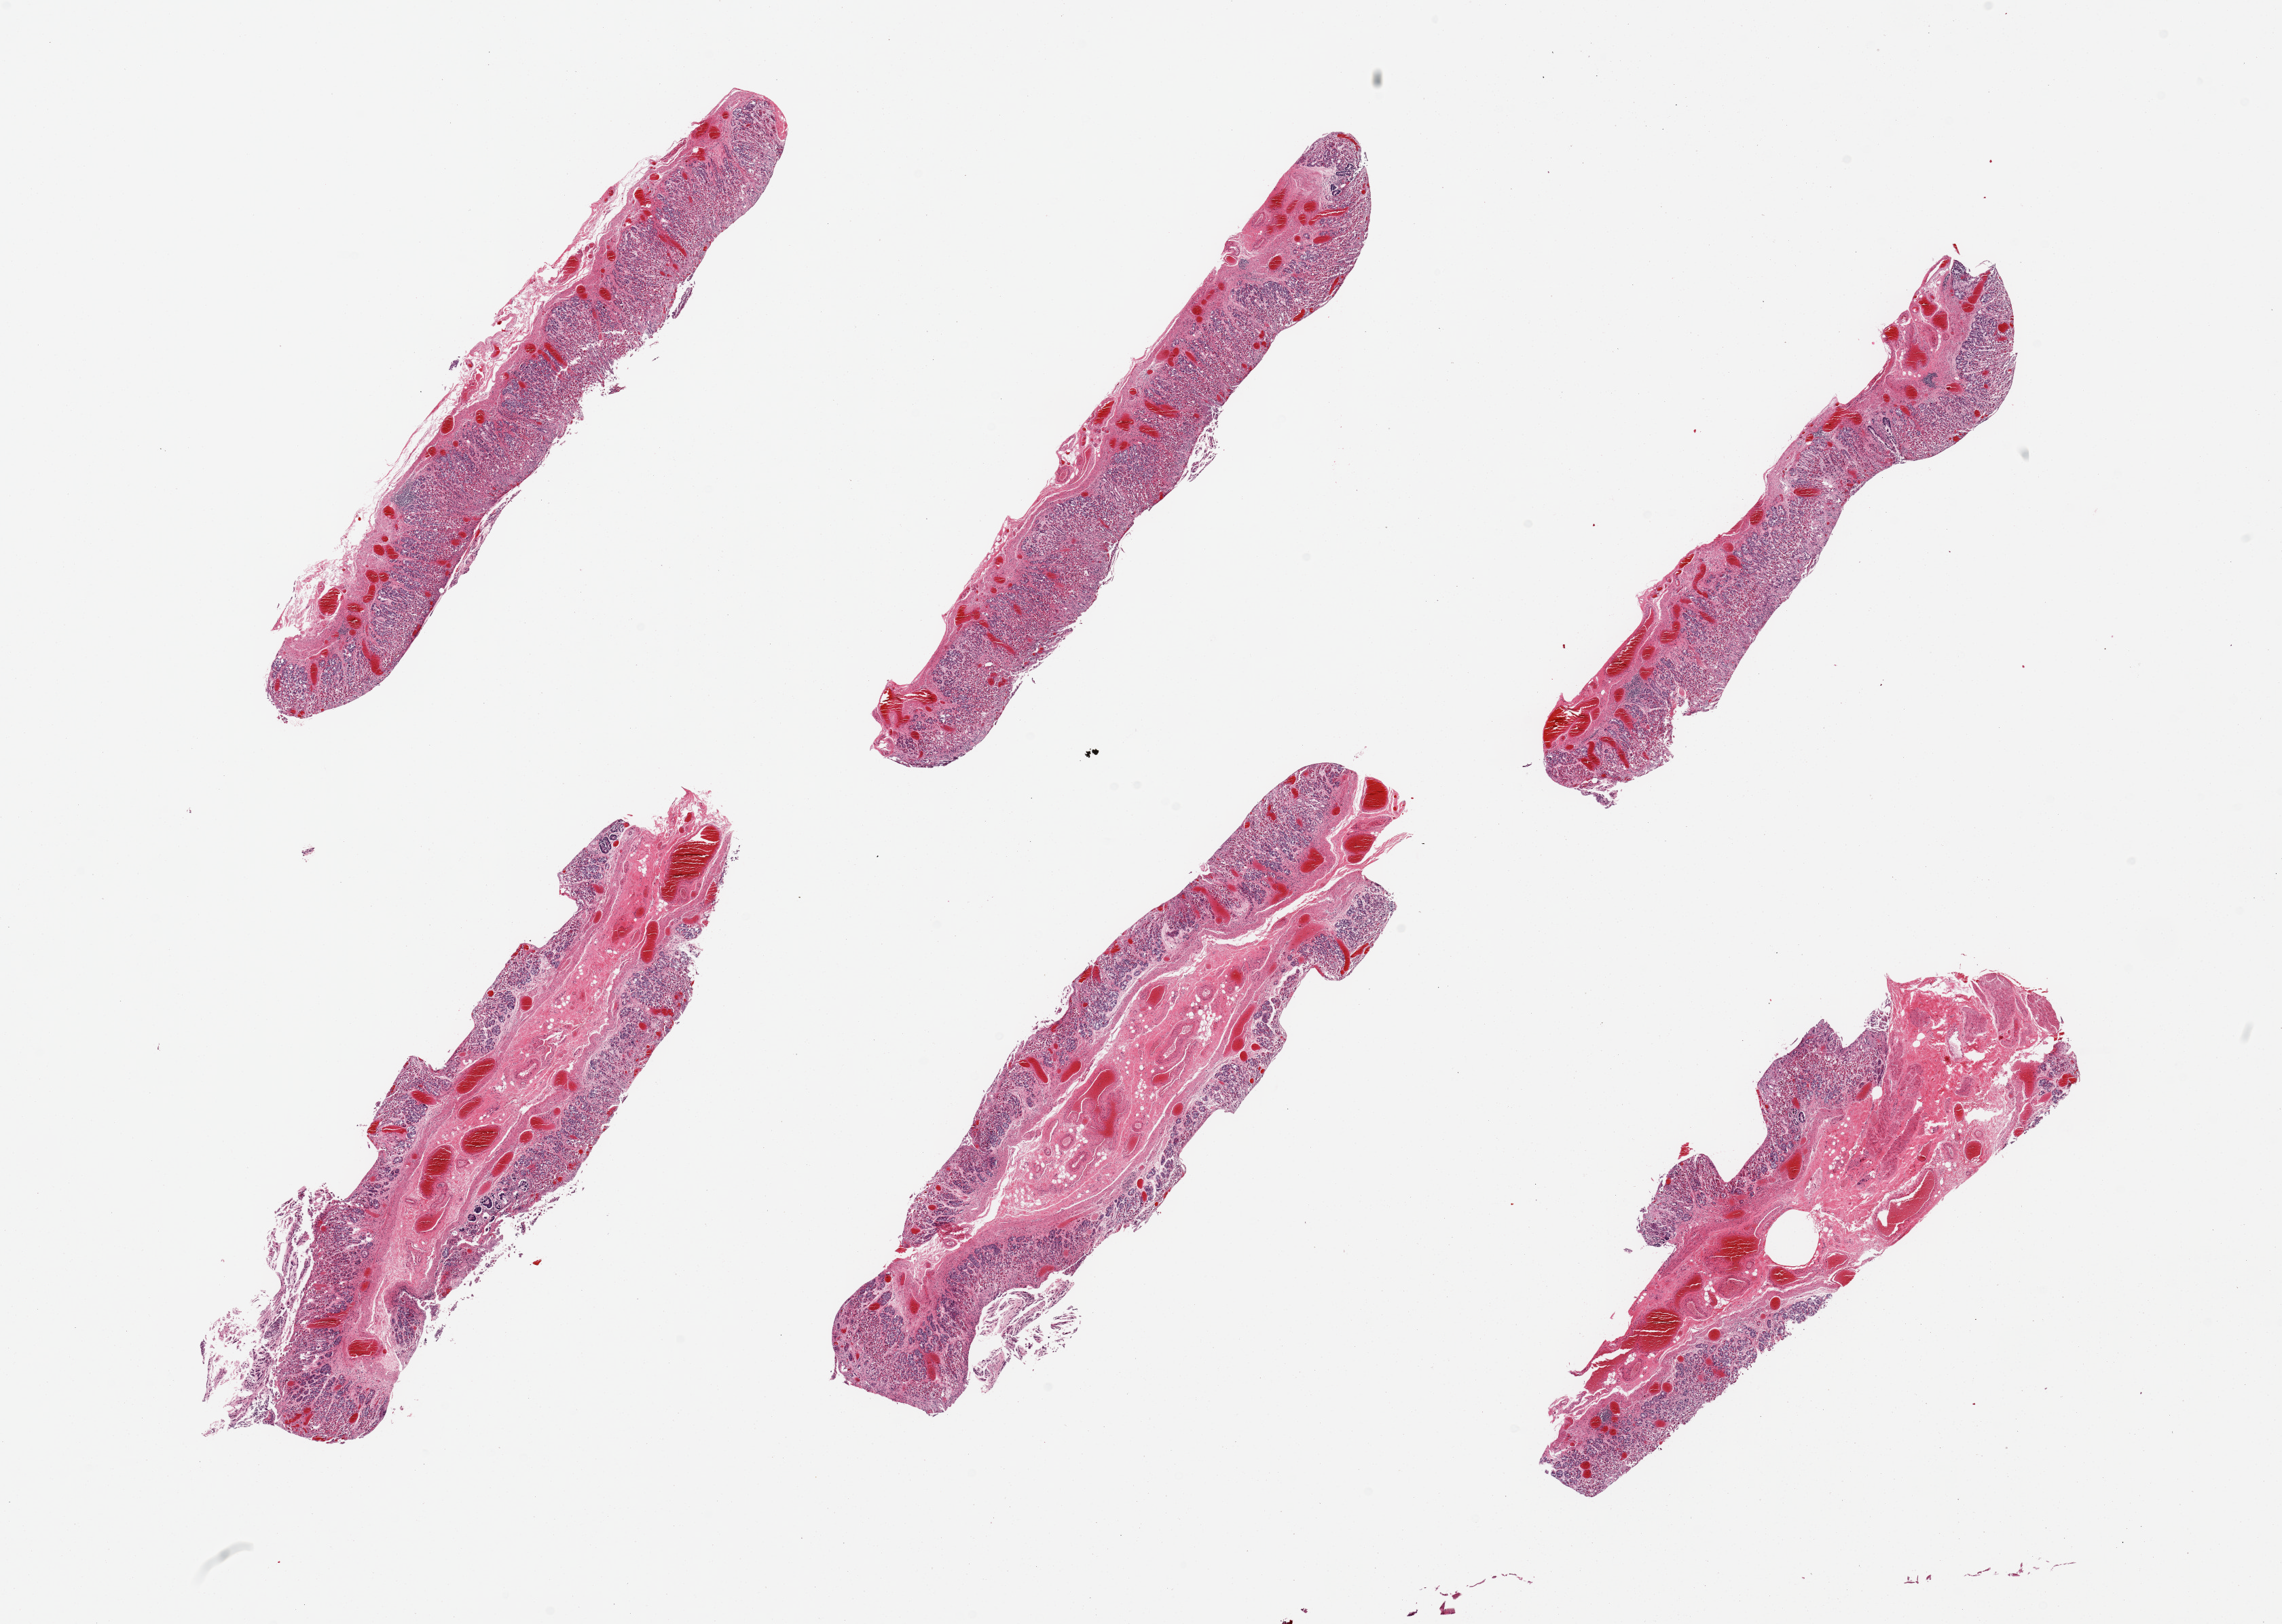
Haematoxylin and eosin whole-slide image, whole scanned area (about 26.6 x 18.9 mm, slide scanned at 20x) shown as a low-resolution overview; PAXgene-fixed, paraffin-embedded tissue; section of stomach (target tissue); donor tissue sample. Male donor.
Pathologist's review note for this sample: 6 pieces, mucosa up to ~50% thickness, advanced autolysis.